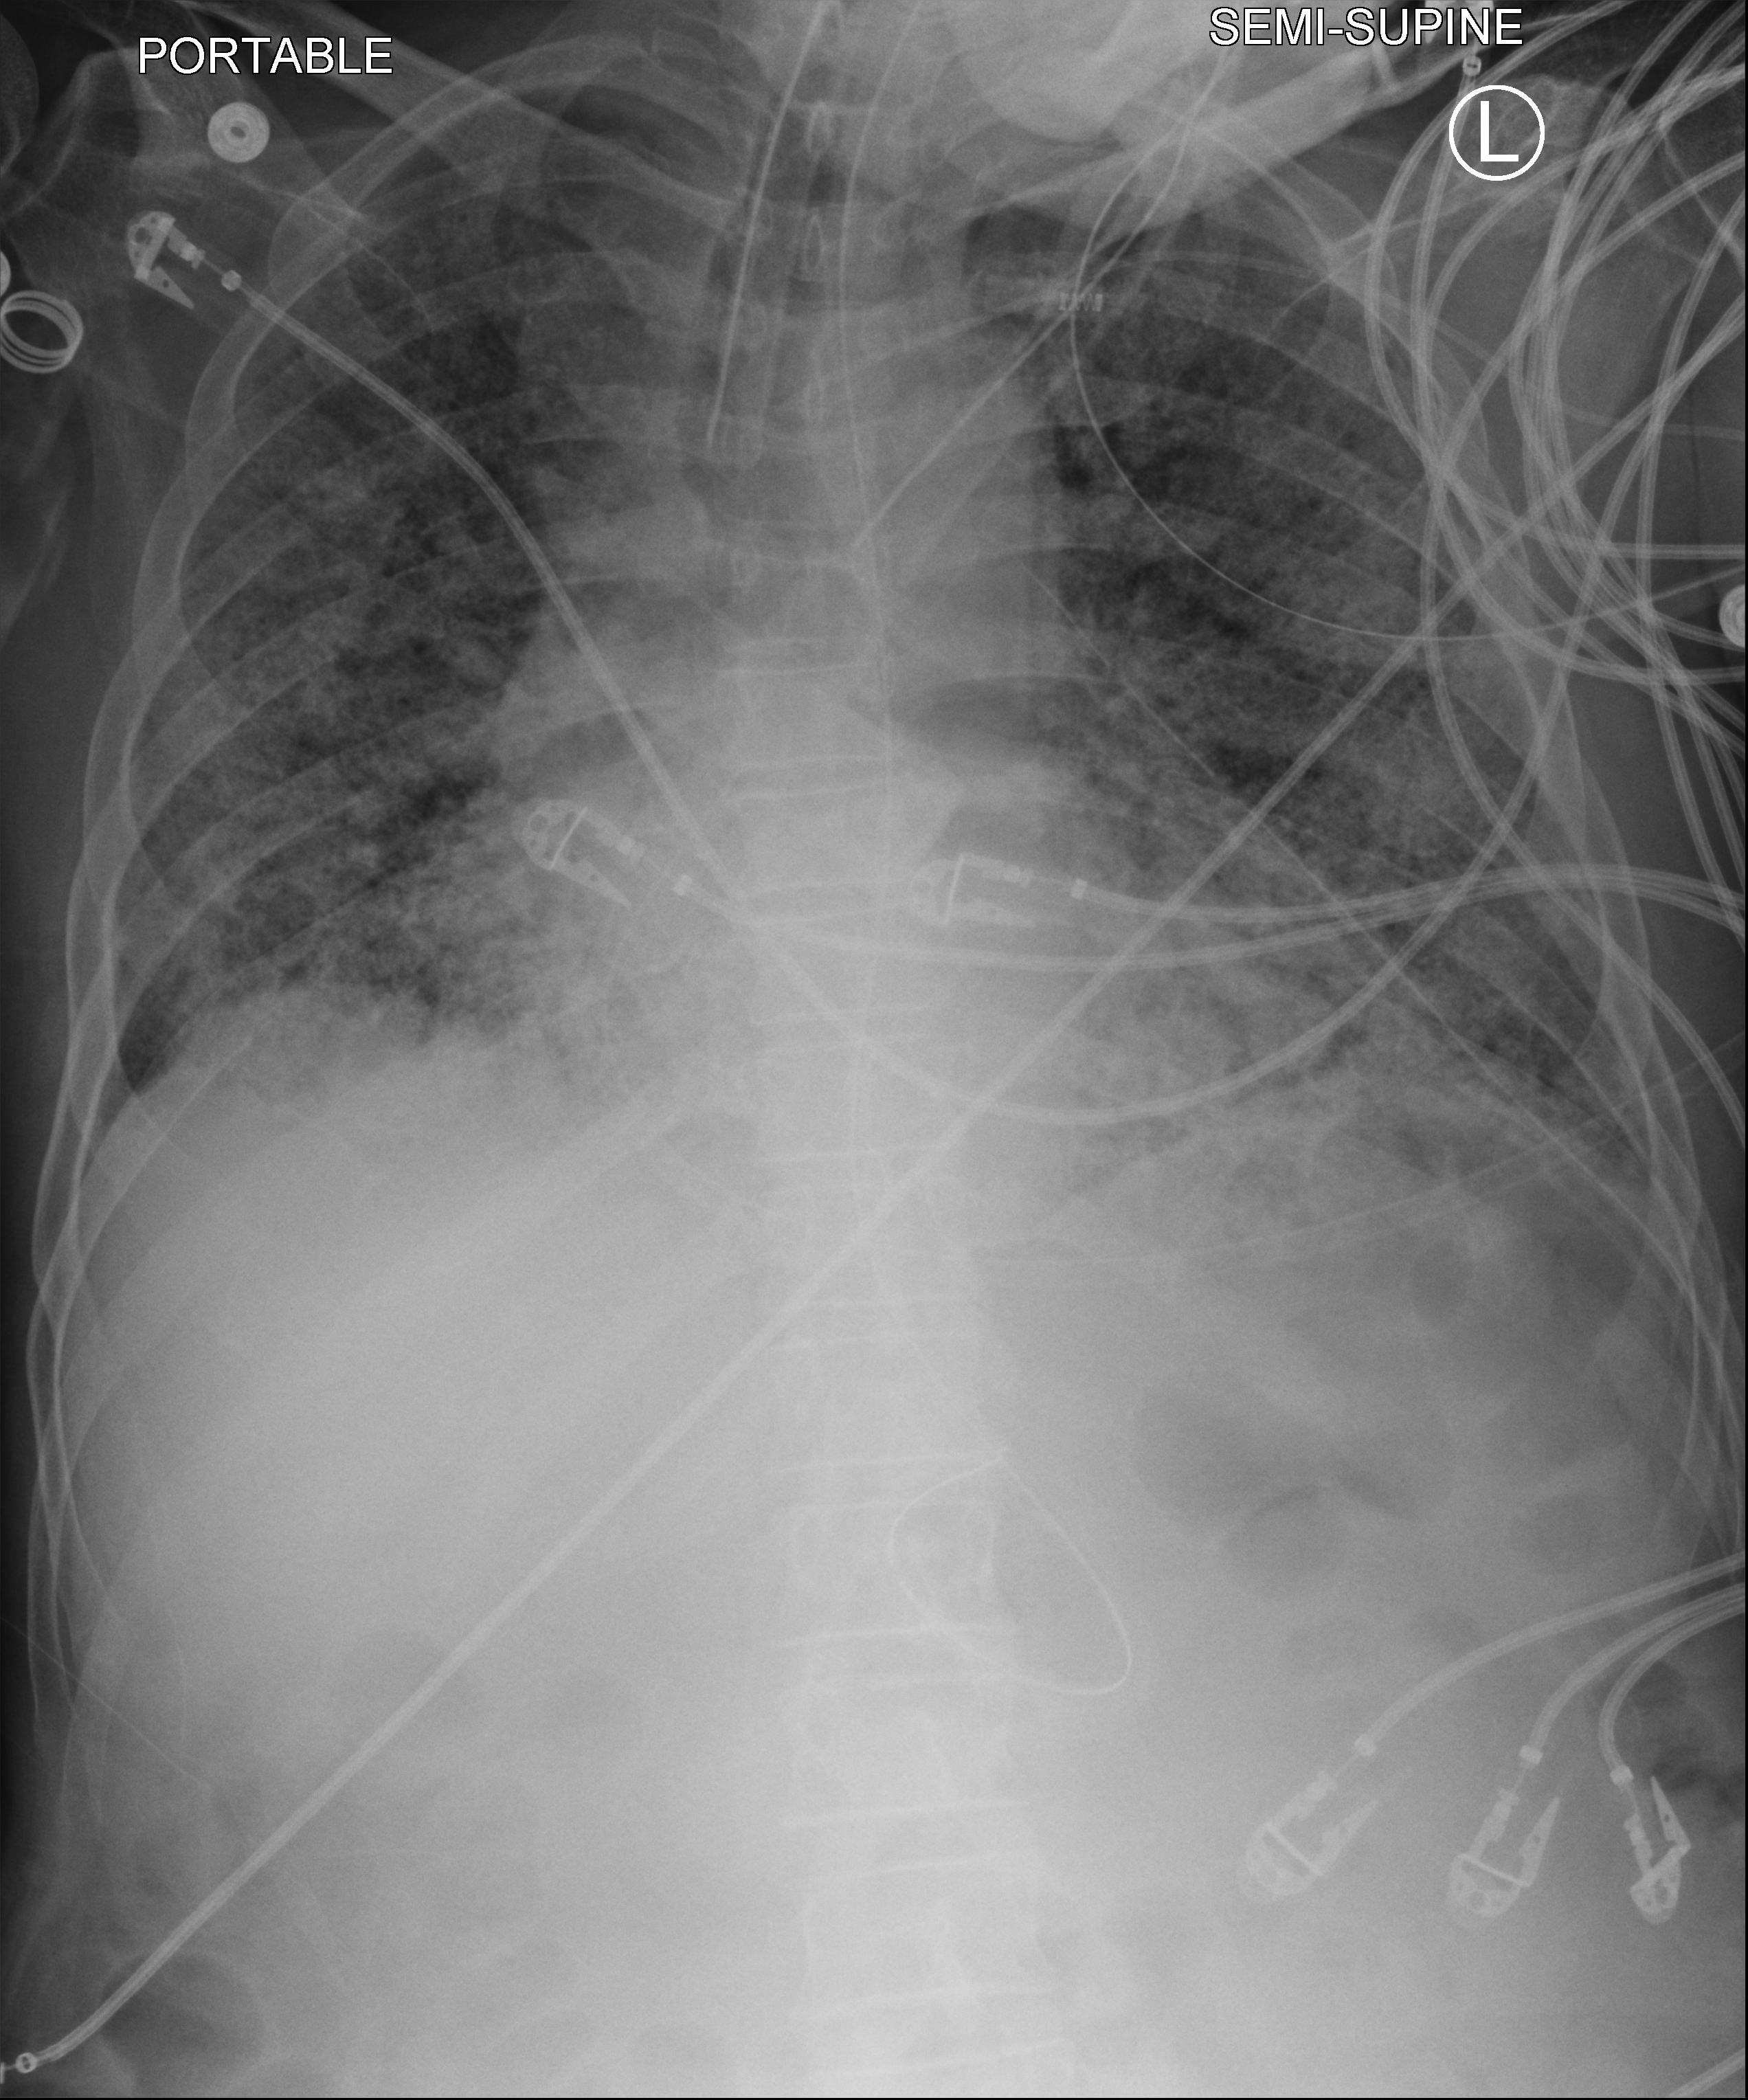
Chest X-ray (portable); anteroposterior (AP) projection. Male patient hospitalised with COVID-19, age 60–74 years.
Admission-level facts for this patient (not findings on this image; timing relative to this image not recorded): mechanically ventilated during this hospital stay: yes.